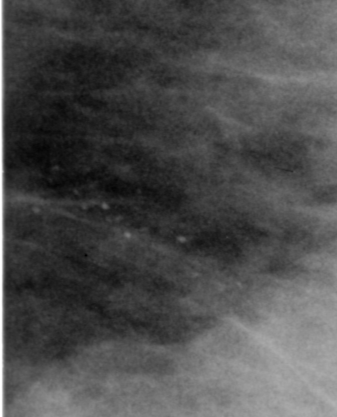
Region of interest cut from a scanned film mammogram (one marked finding); left breast; MLO view.
- Finding: calcifications, morphology pleomorphic, distribution clustered; BI-RADS assessment category 0 (incomplete: needs additional imaging); pathology result (as recorded, not read from the image): malignant.